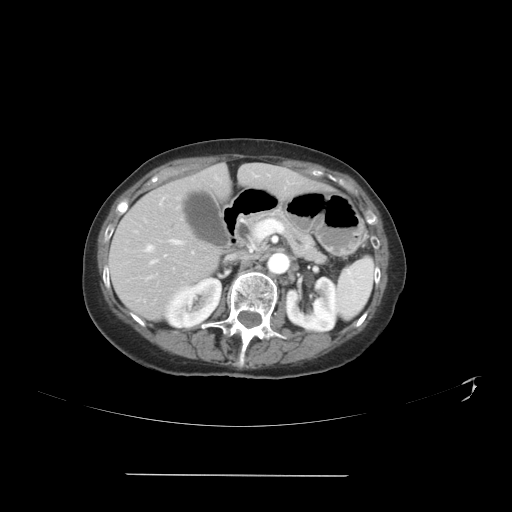
Contrast-enhanced abdominal CT, one axial slice. Slice 20 of 41 in the series (ordered by position). 120 kVp. Intravenous contrast given. Soft-tissue window (W 400 / L 40 HU). 512 × 512 image matrix, field of view 431 × 431 mm. Female patient, age 74 years. From the clinical record (not read from this slice): diagnosis: colorectal cancer liver metastases, imaged before liver resection; multiple liver metastases: yes; largest metastasis: 3.3 cm; disease in both lobes: yes.
Outlined on this slice (outlined manually by an expert reader):
- hepatic veins: box from (x=144, y=207) to (x=178, y=265) px
- liver: (x=110, y=165)–(x=317, y=319)
- planned liver remnant (the part of the liver to remain after resection): (x=118, y=165)–(x=316, y=251)
- portal vein (with intrahepatic branches): (x=171, y=239)–(x=182, y=244)